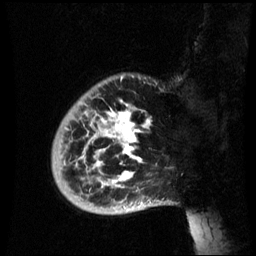
Breast MRI (dynamic contrast-enhanced), one sagittal slice. Slice 11 of 60 in the series (ordered by position). Dynamic contrast-enhanced series, image 2 of 3 at this slice position (ordered by acquisition). 1.5 T. TE 4.2 ms, TR 8.9 ms. 256 × 256 image matrix. Female patient, age 35 years. From the clinical record (not read from this slice): setting: breast cancer imaged before/during neoadjuvant chemotherapy; receptor status: HR-positive, HER2-negative.
Outlined on this slice (semi-automatically segmented with operator editing):
- analysis volume of interest (the breast-tissue region the enhancement analysis was run in; not a lesion): bounding box (x1, y1, x2, y2) in pixels: (51, 74, 164, 215)
- tumour enhancement mask (voxels above the 70 % enhancement threshold inside the analysis volume of interest): (76, 104, 141, 185)